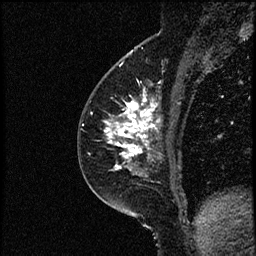
Breast MRI (dynamic contrast-enhanced), one sagittal slice; dynamic contrast-enhanced study with each time point stored as its own series, time point 2 of 3 at this slice position (early post-contrast, ordered by acquisition time); 1.5 T; TE 4.2 ms, TR 17.6 ms; 2 mm slice thickness; 256 × 256 image matrix. Female patient, age 49 years. Case-level facts recorded for this patient, not image findings: setting: breast cancer imaged before/during neoadjuvant chemotherapy; receptor status: HER2-positive.
Outlined on this slice (semi-automatically segmented with operator editing):
- analysis volume of interest (the breast-tissue region the enhancement analysis was run in; not a lesion): bounding box <85,65,182,175> (left, top, right, bottom; pixels)
- tumour enhancement mask (voxels above the 100 % enhancement threshold inside the analysis volume of interest): <104,98,160,175>